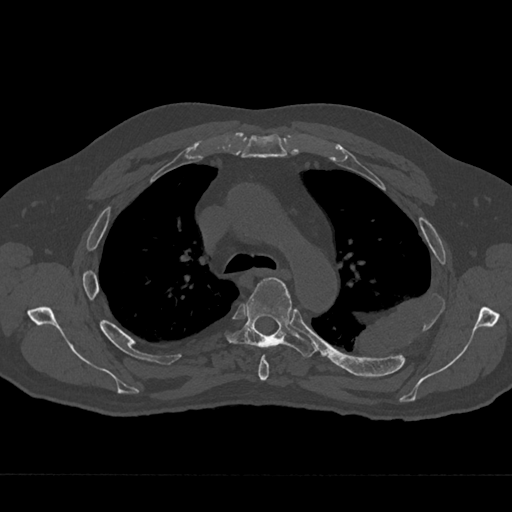
CT including the spine, one axial slice. Position 485 of 797 along the scan axis. 120 kVp. Bone window (W 1800 / L 400 HU). 512 × 512 image matrix, field of view 377 × 377 mm. Male patient, age 75 years. From the clinical record (not read from this slice): primary cancer: renal; vertebrae with lytic lesions (as recorded): T4.
Outlined on this slice (semi-automatically segmented with operator editing):
- T4 vertebra: bounding box <258,354,269,381> (left, top, right, bottom; pixels)
- T5 vertebra: <225,278,317,358>